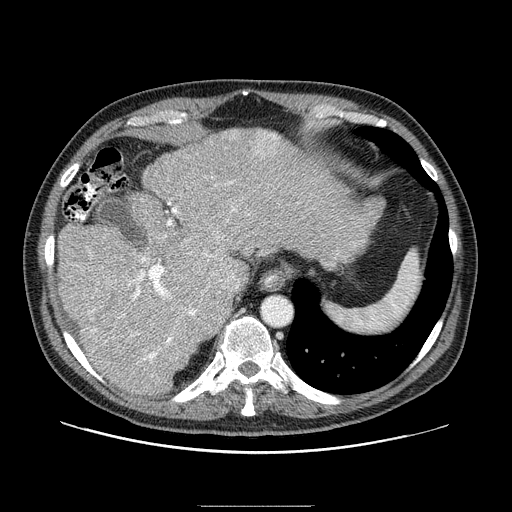
Contrast-enhanced abdominal CT (liver protocol), one axial slice; slice 65 of 99 in the series (ordered by position); reconstruction kernel STANDARD; one of 2 acquisitions stored at this slice position; soft-tissue window (W 400 / L 40 HU); 2.5 mm slice thickness; 512 × 512 image matrix, field of view 400 × 400 mm. Case-level facts recorded for this patient, not image findings: diagnosis: hepatocellular carcinoma (patient treated with transarterial chemoembolisation; whether this scan precedes or follows treatment is not stated here); TNM stage (as recorded): Stage-II; Child-Pugh class: A; tumour differentiation: well differentiated; tumour size: 3.2 cm.
Outlined on this slice (semi-automatic segmentation, software-assisted and operator-edited):
- abdominal aorta: bounding box (x1, y1, x2, y2) in pixels: (263, 297, 292, 325)
- liver parenchyma outside the tumour (the mass and vessels are separate outlines, so this box may not span the whole liver): (58, 128, 384, 394)
- mass: (251, 129, 284, 160)
- liver vessels: (89, 177, 250, 377)